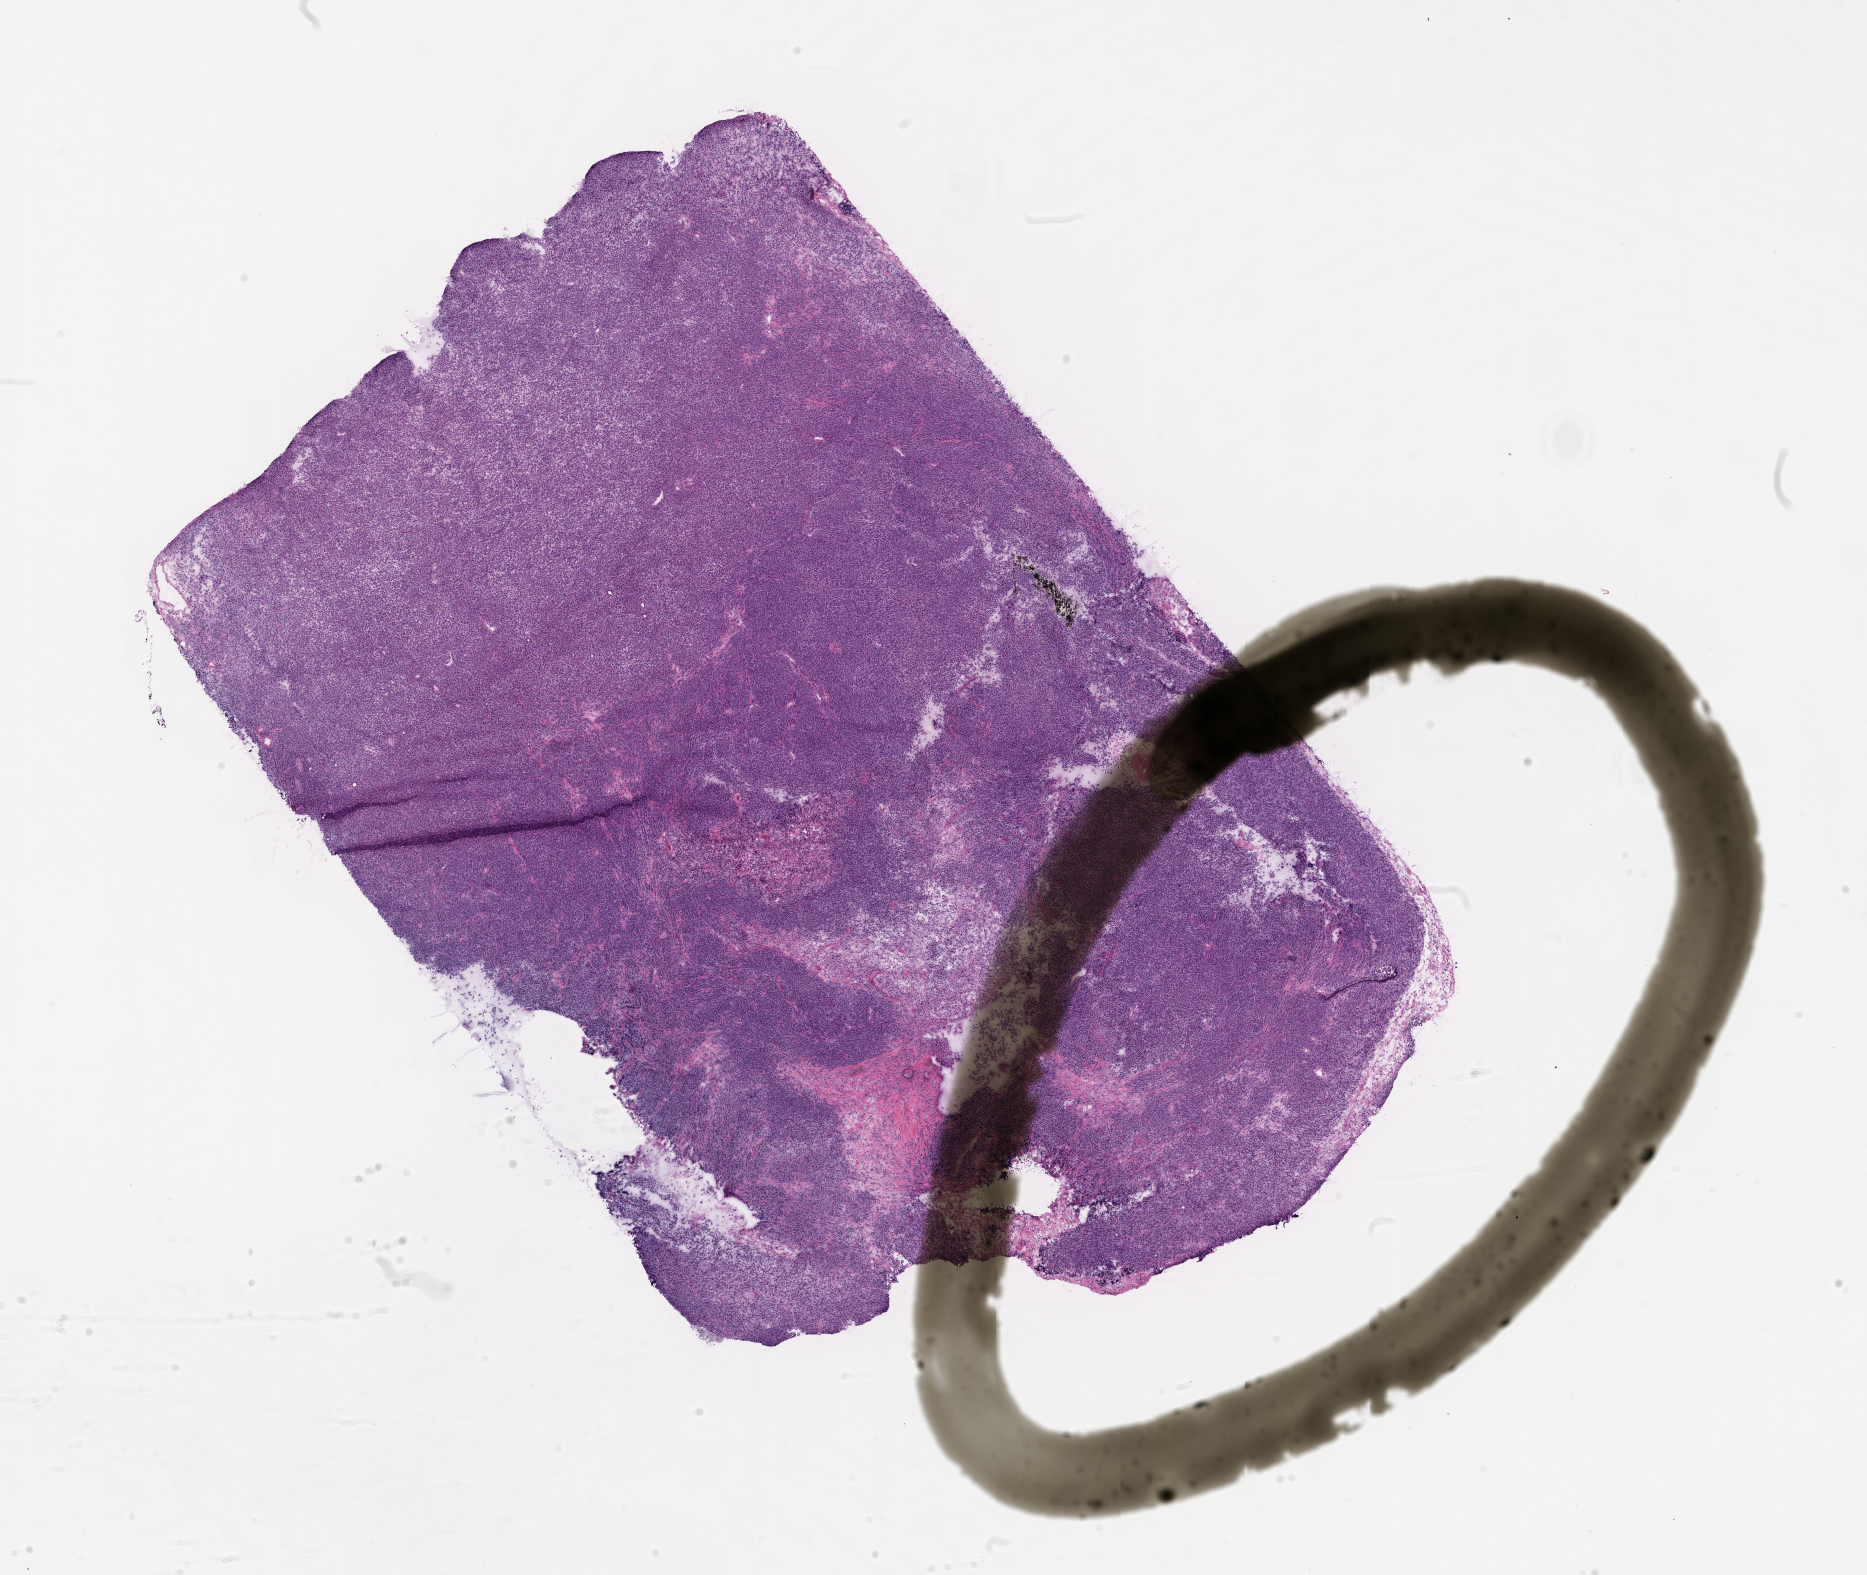
Whole-slide image, hematoxylin and eosin (H&E): patient-derived xenograft (human tumor grown in a mouse), shown as a low-resolution overview of the whole scanned area (about 15.0 x 12.7 mm), formalin-fixed, paraffin-embedded (FFPE) tissue, tumor site category: skin.
Originating patient diagnosis: Melanoma.